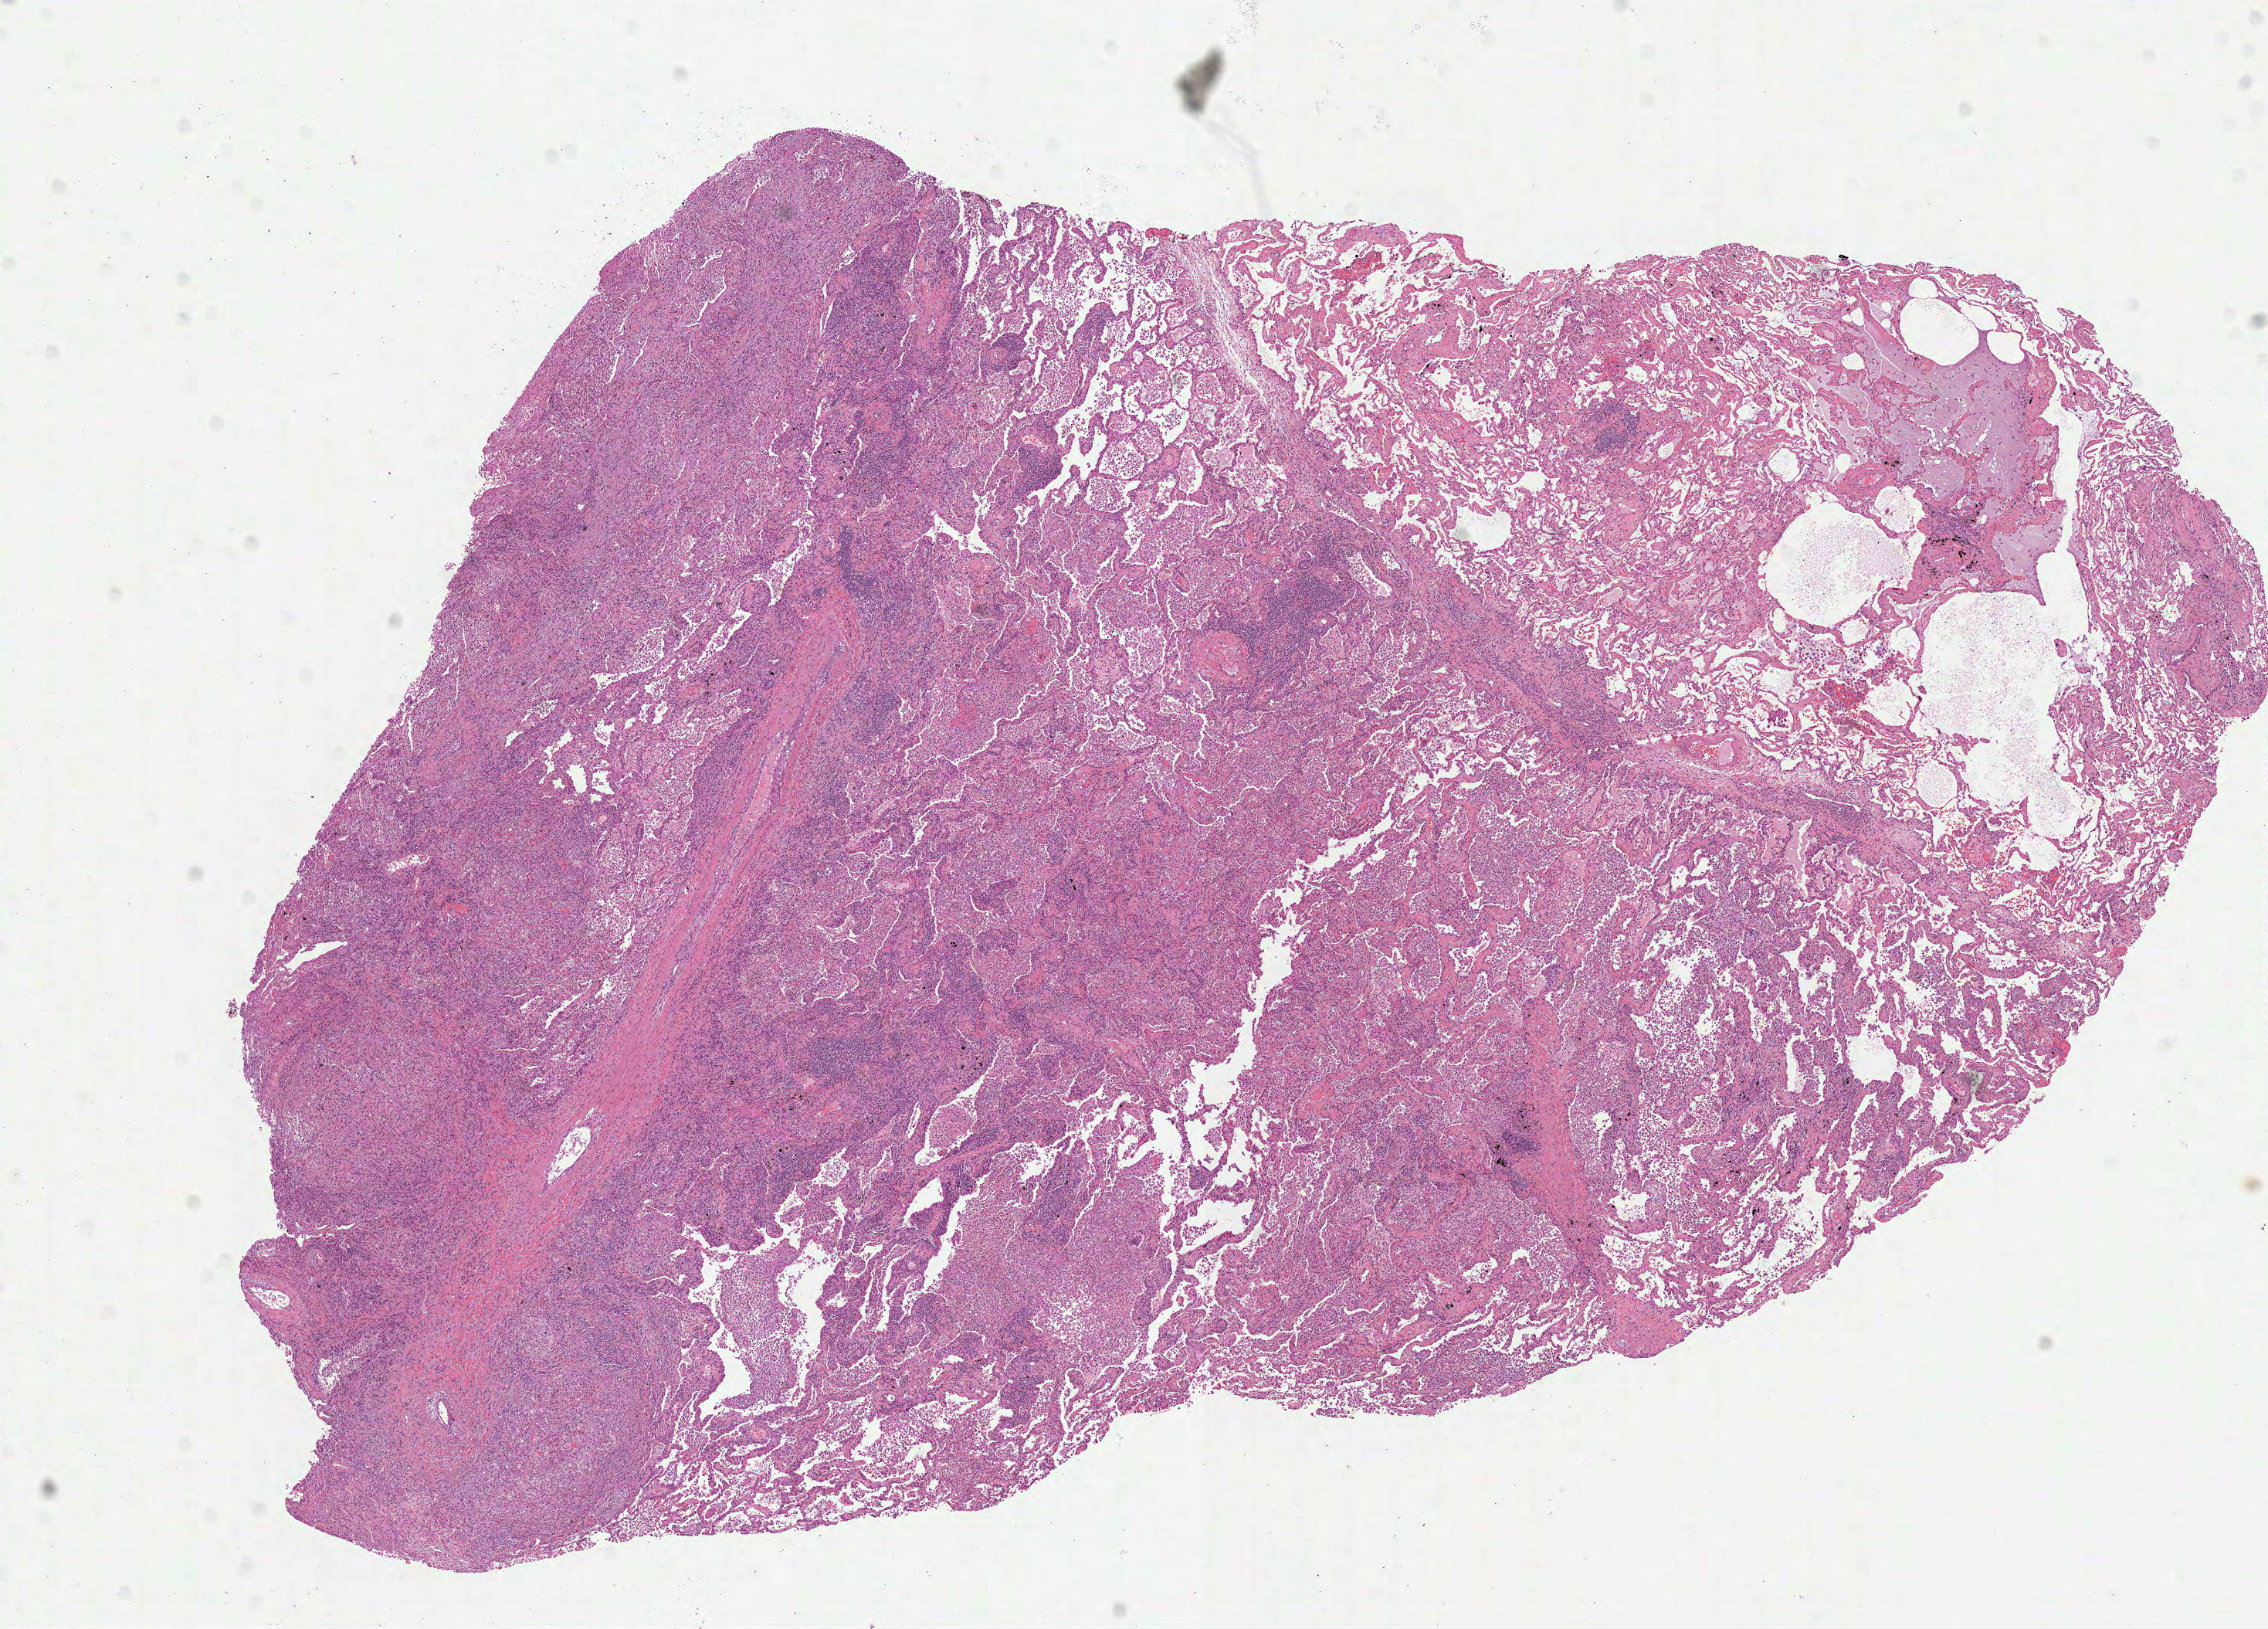
Digitized H&E-stained tissue section (whole slide) — a low-resolution overview of the entire scanned area, about 11.8 x 8.5 mm; FFPE section; primary tumour sample from the lung. Patient: female, age at initial diagnosis 58 years.
Diagnosis: Squamous cell carcinoma, NOS (upper lobe, lung).